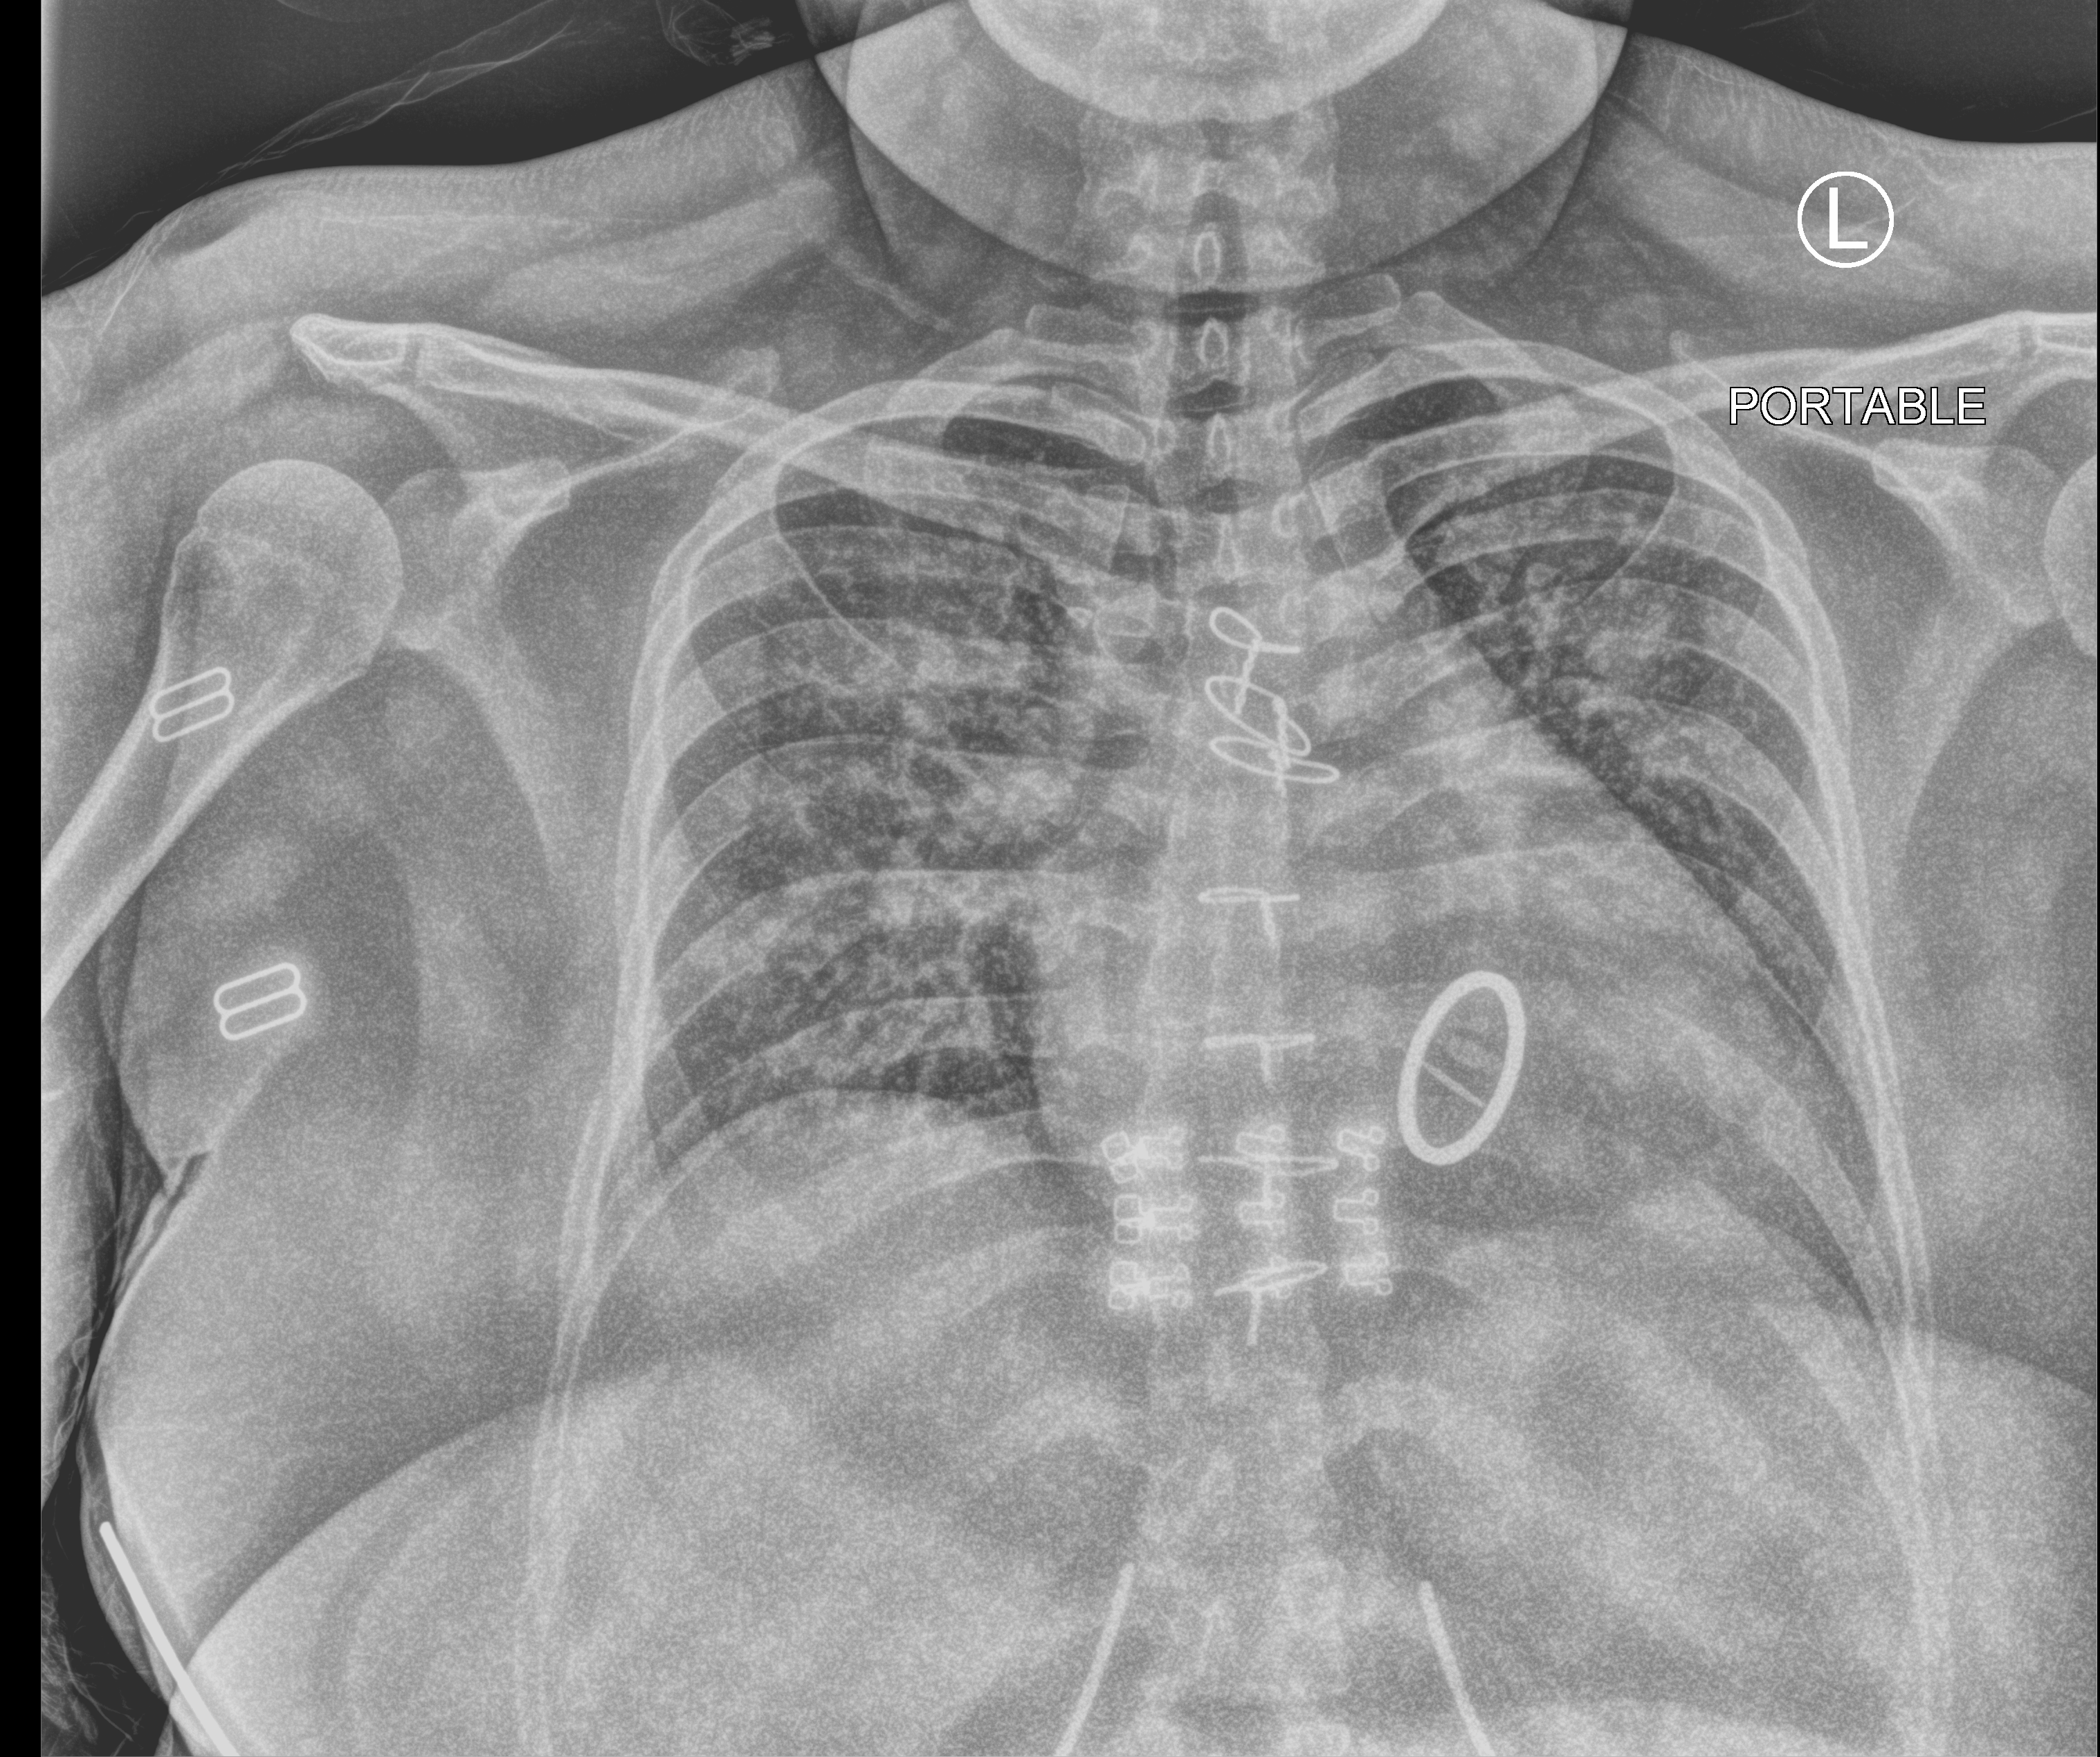
Portable chest radiograph; anteroposterior (AP) projection. Female patient hospitalised with COVID-19, age 18–59 years.
Hospital-stay facts (about this admission, not read from this image; timing relative to this image not recorded):
- smoking status (admission record): former
- hypertension (admission record): no